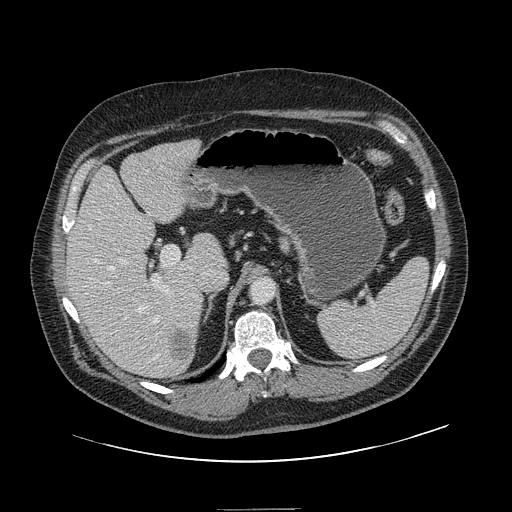
Contrast-enhanced abdominal CT, one axial slice. Intravenous contrast given. Soft-tissue window (W 400 / L 40 HU). 2.5 mm slice thickness. 512 × 512 image matrix, field of view 451 × 451 mm. Male patient, age 61 years. From the clinical record (not read from this slice): diagnosis: colorectal cancer liver metastases, imaged before liver resection; multiple liver metastases: yes; largest metastasis: 2.6 cm; disease in both lobes: yes.
Structures marked on this image (outlined manually by an expert reader):
- hepatic veins: bounding box <88,211,159,360> (left, top, right, bottom; pixels)
- liver: <68,141,223,378>
- planned liver remnant (the part of the liver to remain after resection): <68,146,223,365>
- portal vein (with intrahepatic branches): <104,185,169,293>
- liver metastasis: <172,333,196,364>